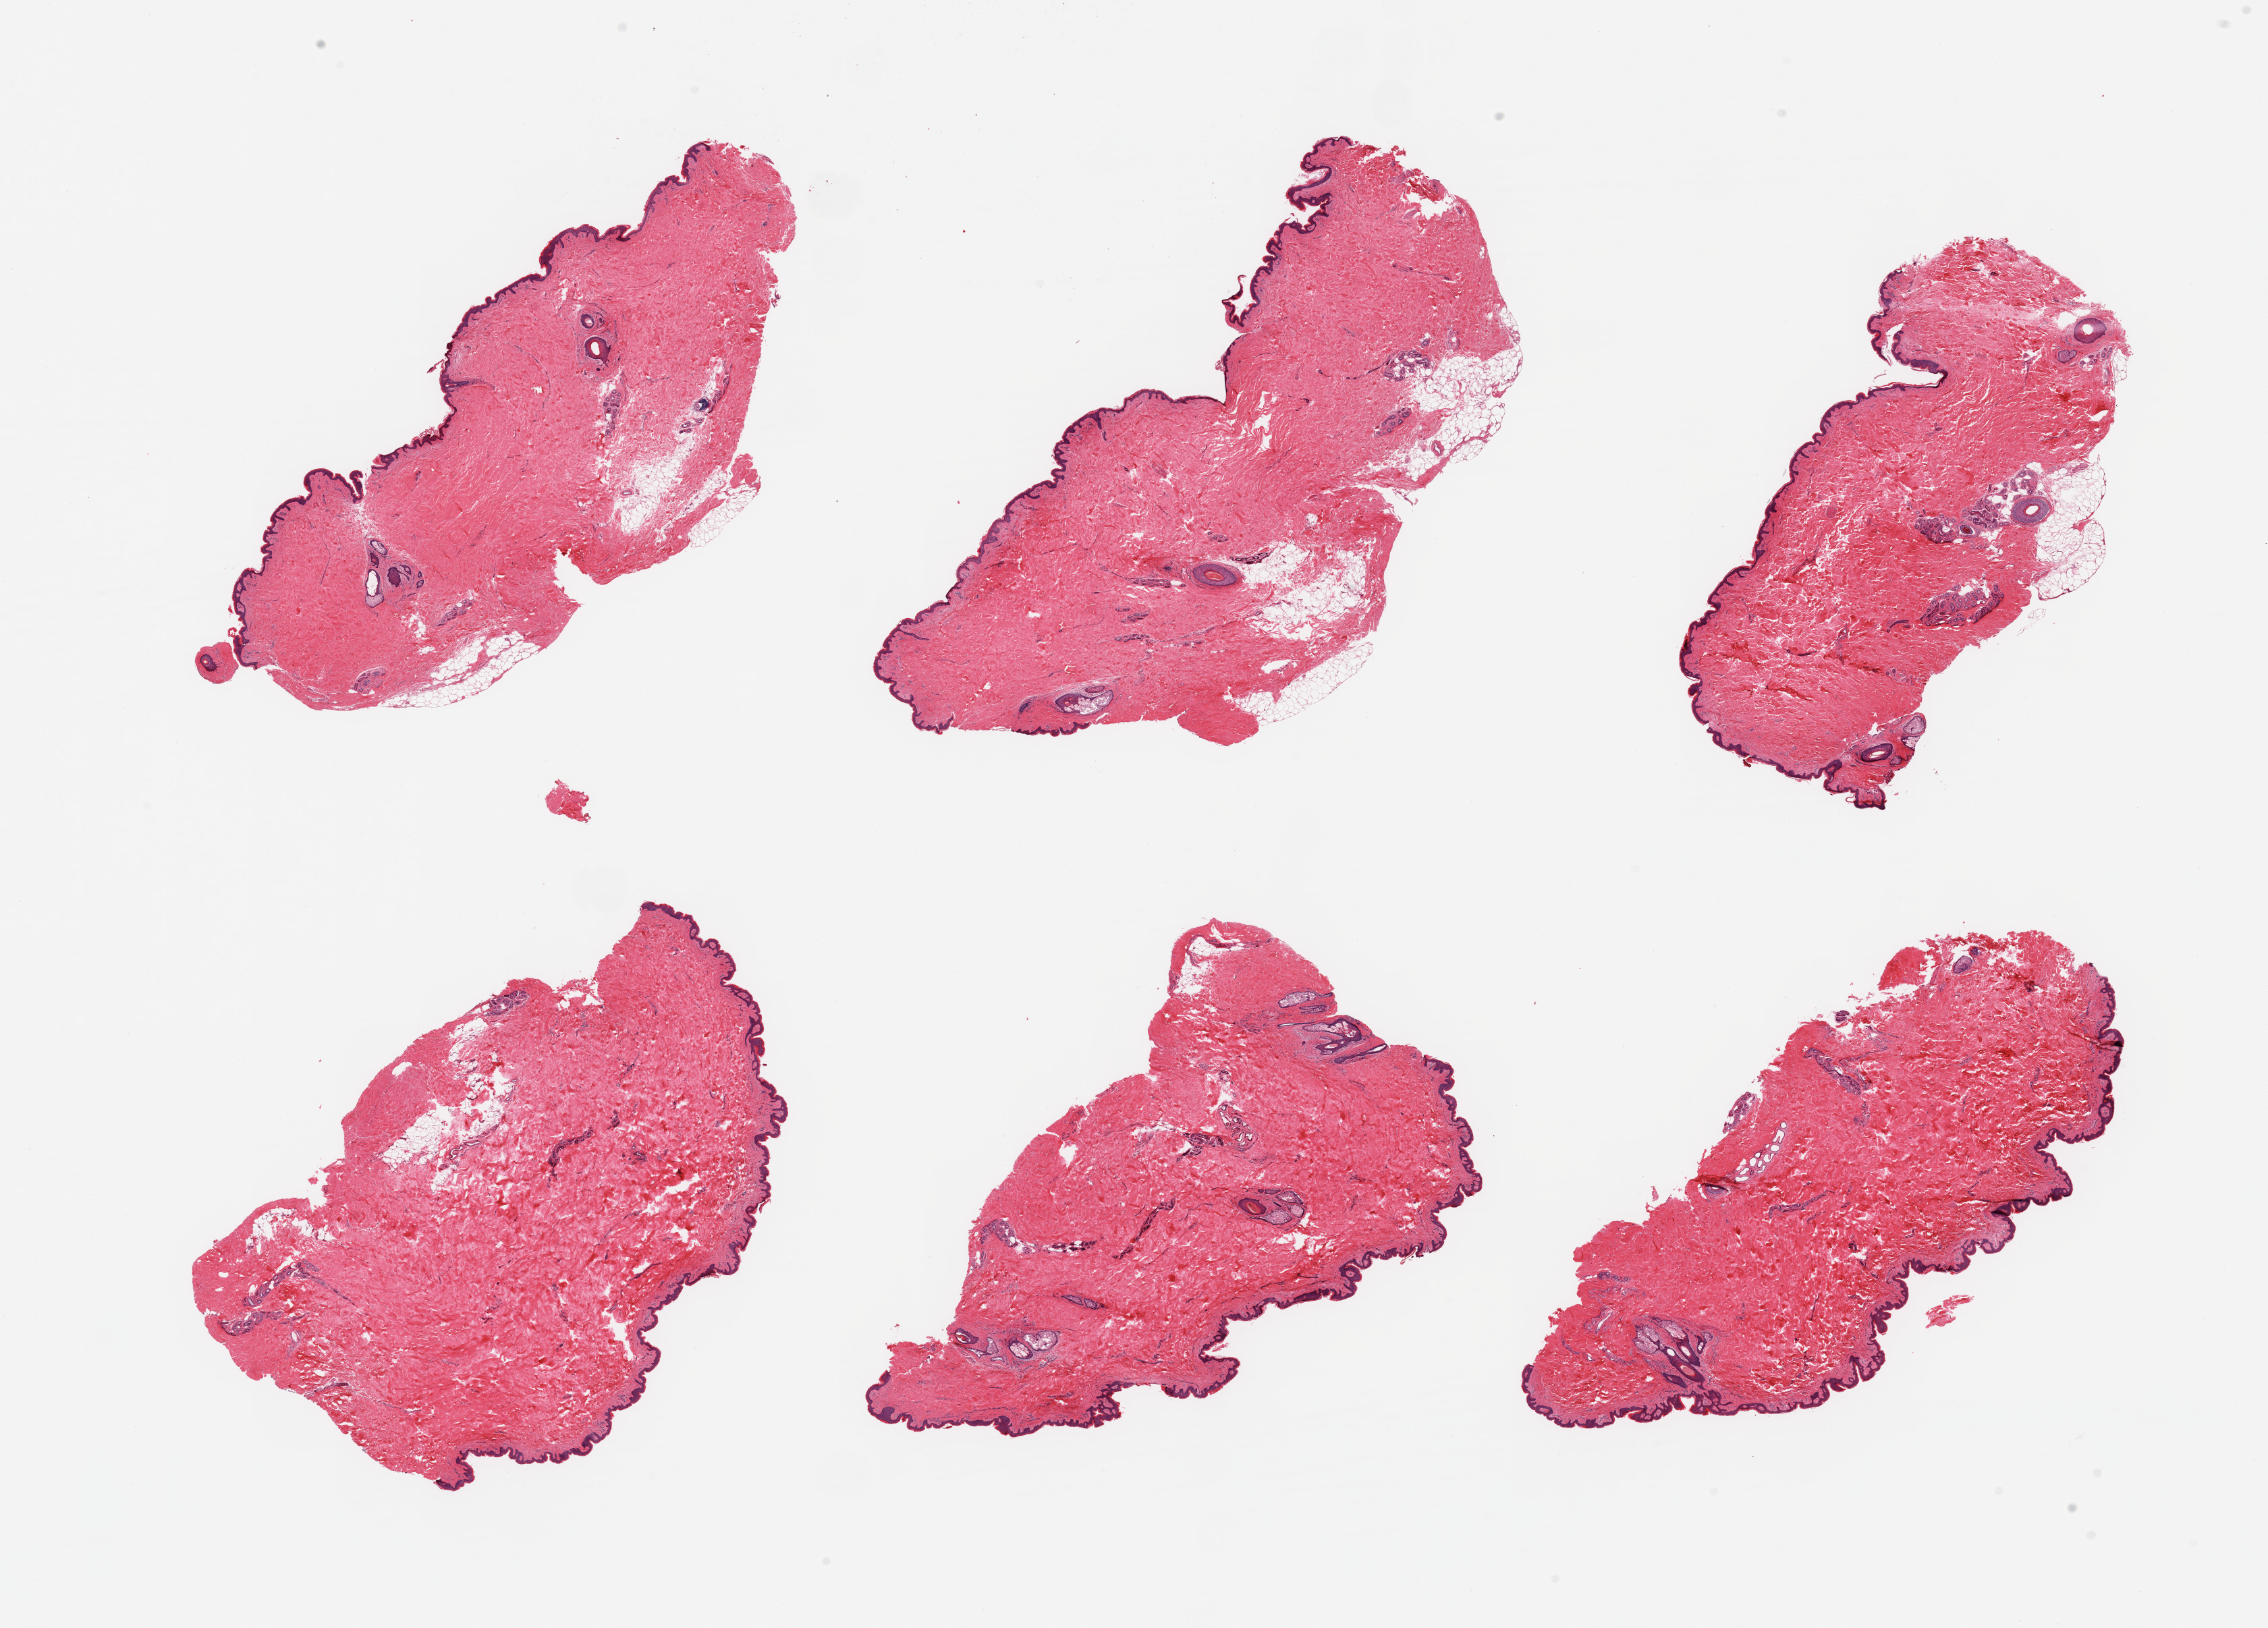
Digitized haematoxylin and eosin-stained section, a low-resolution overview of the entire scanned area, about 26.6 x 19.1 mm (slide scanned at 20x); PAXgene-fixed paraffin-embedded (PFPE) section; sampled site (target tissue): skin of suprapubic region; donor tissue sample.
Review note (as recorded): 6 pieces, dermal fat focally present; ~1mm; squamous epithelium is ~40-50 microns.